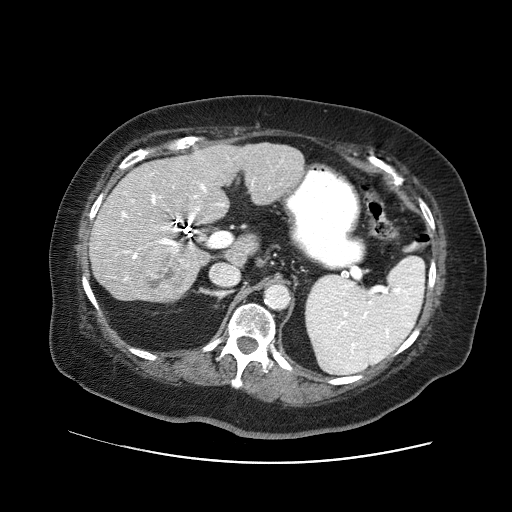
Contrast-enhanced abdominal CT (liver protocol), one axial slice; position 27 of 71 along the scan axis; soft-tissue window (W 400 / L 40 HU); 2.5 mm slice thickness; 512 × 512 image matrix. Case-level facts recorded for this patient, not image findings: diagnosis: hepatocellular carcinoma (patient treated with transarterial chemoembolisation; whether this scan precedes or follows treatment is not stated here); TNM stage (as recorded): Stage-II; Child-Pugh class: A; tumour differentiation: poorly differentiated; tumour size: 5 cm.
Outlined on this slice (semi-automatically segmented with operator editing):
- liver parenchyma outside the tumour (the mass and vessels are separate outlines, so this box may not span the whole liver): bounding box (x1, y1, x2, y2) in pixels: (88, 142, 304, 300)
- mass: (142, 250, 187, 296)
- liver vessels: (121, 160, 282, 280)